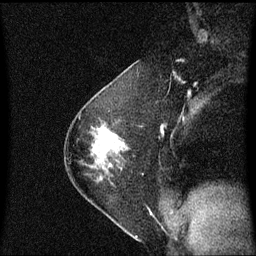
Breast MRI (dynamic contrast-enhanced), one sagittal slice. Position 38 of 60 along the scan axis. Dynamic contrast-enhanced series, image 2 of 3 at this slice position (ordered by acquisition). 1.5 T. TE 4.2 ms, TR 8.4 ms. 256 × 256 image matrix, field of view 210 × 210 mm. Female patient, age 54 years. Case-level facts recorded for this patient, not image findings: setting: breast cancer imaged before/during neoadjuvant chemotherapy; receptor status: HER2-positive.
Structures marked on this image (semi-automatically segmented with operator editing):
- analysis volume of interest (the breast-tissue region the enhancement analysis was run in; not a lesion): bounding box [x1, y1, x2, y2] px = [87, 124, 127, 182]
- tumour enhancement mask (voxels above the 70 % enhancement threshold inside the analysis volume of interest): [103, 131, 125, 145]